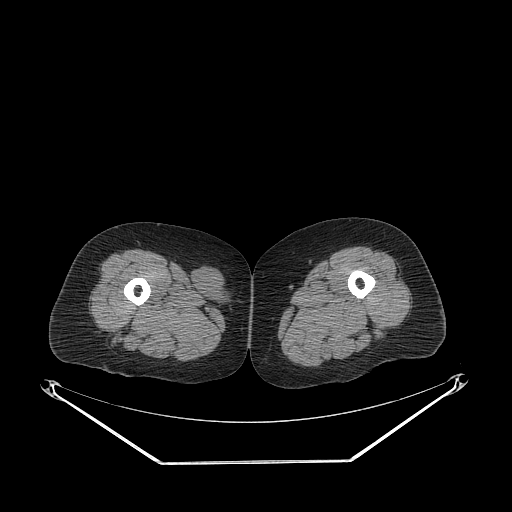
CT of an extremity soft-tissue mass (from a PET/CT study), one axial slice. Slice 240 of 311 in the series (ordered by position). 140 kVp. Soft-tissue window (W 400 / L 40 HU). 3.75 mm slice thickness. 512 × 512 image matrix, field of view 500 × 500 mm. Female patient. From the clinical record (not read from this slice): histological type: leiomyosarcoma; grade: intermediate; site of the primary tumour: parascapusular.
Structures marked on this image (expert contour drawn on MRI and transferred to this co-registered scan by the dataset authors):
- gross tumour volume including surrounding oedema: bounding box <192,263,232,307> (left, top, right, bottom; pixels)
- gross tumour volume (mass): <194,265,225,300>